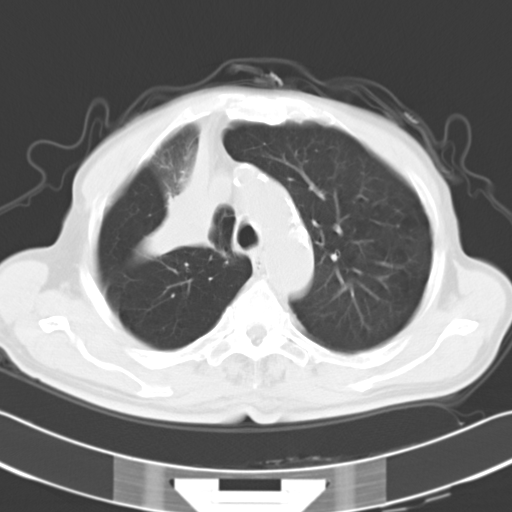
Chest CT, one axial slice; slice 24 of 31 in the series (ordered by position); 120 kVp; lung window (W 1500 / L -600 HU); 10 mm slice thickness; 512 × 512 image matrix, field of view 339 × 339 mm. Male patient, age 73 years. From the clinical record (not read from this slice): clinical TNM (as recorded): T2a N1 M0.
Structures marked on this image (bounding box drawn by a radiologist):
- lung tumour (recorded histology: squamous cell carcinoma): bounding box <136,129,218,265> (left, top, right, bottom; pixels)